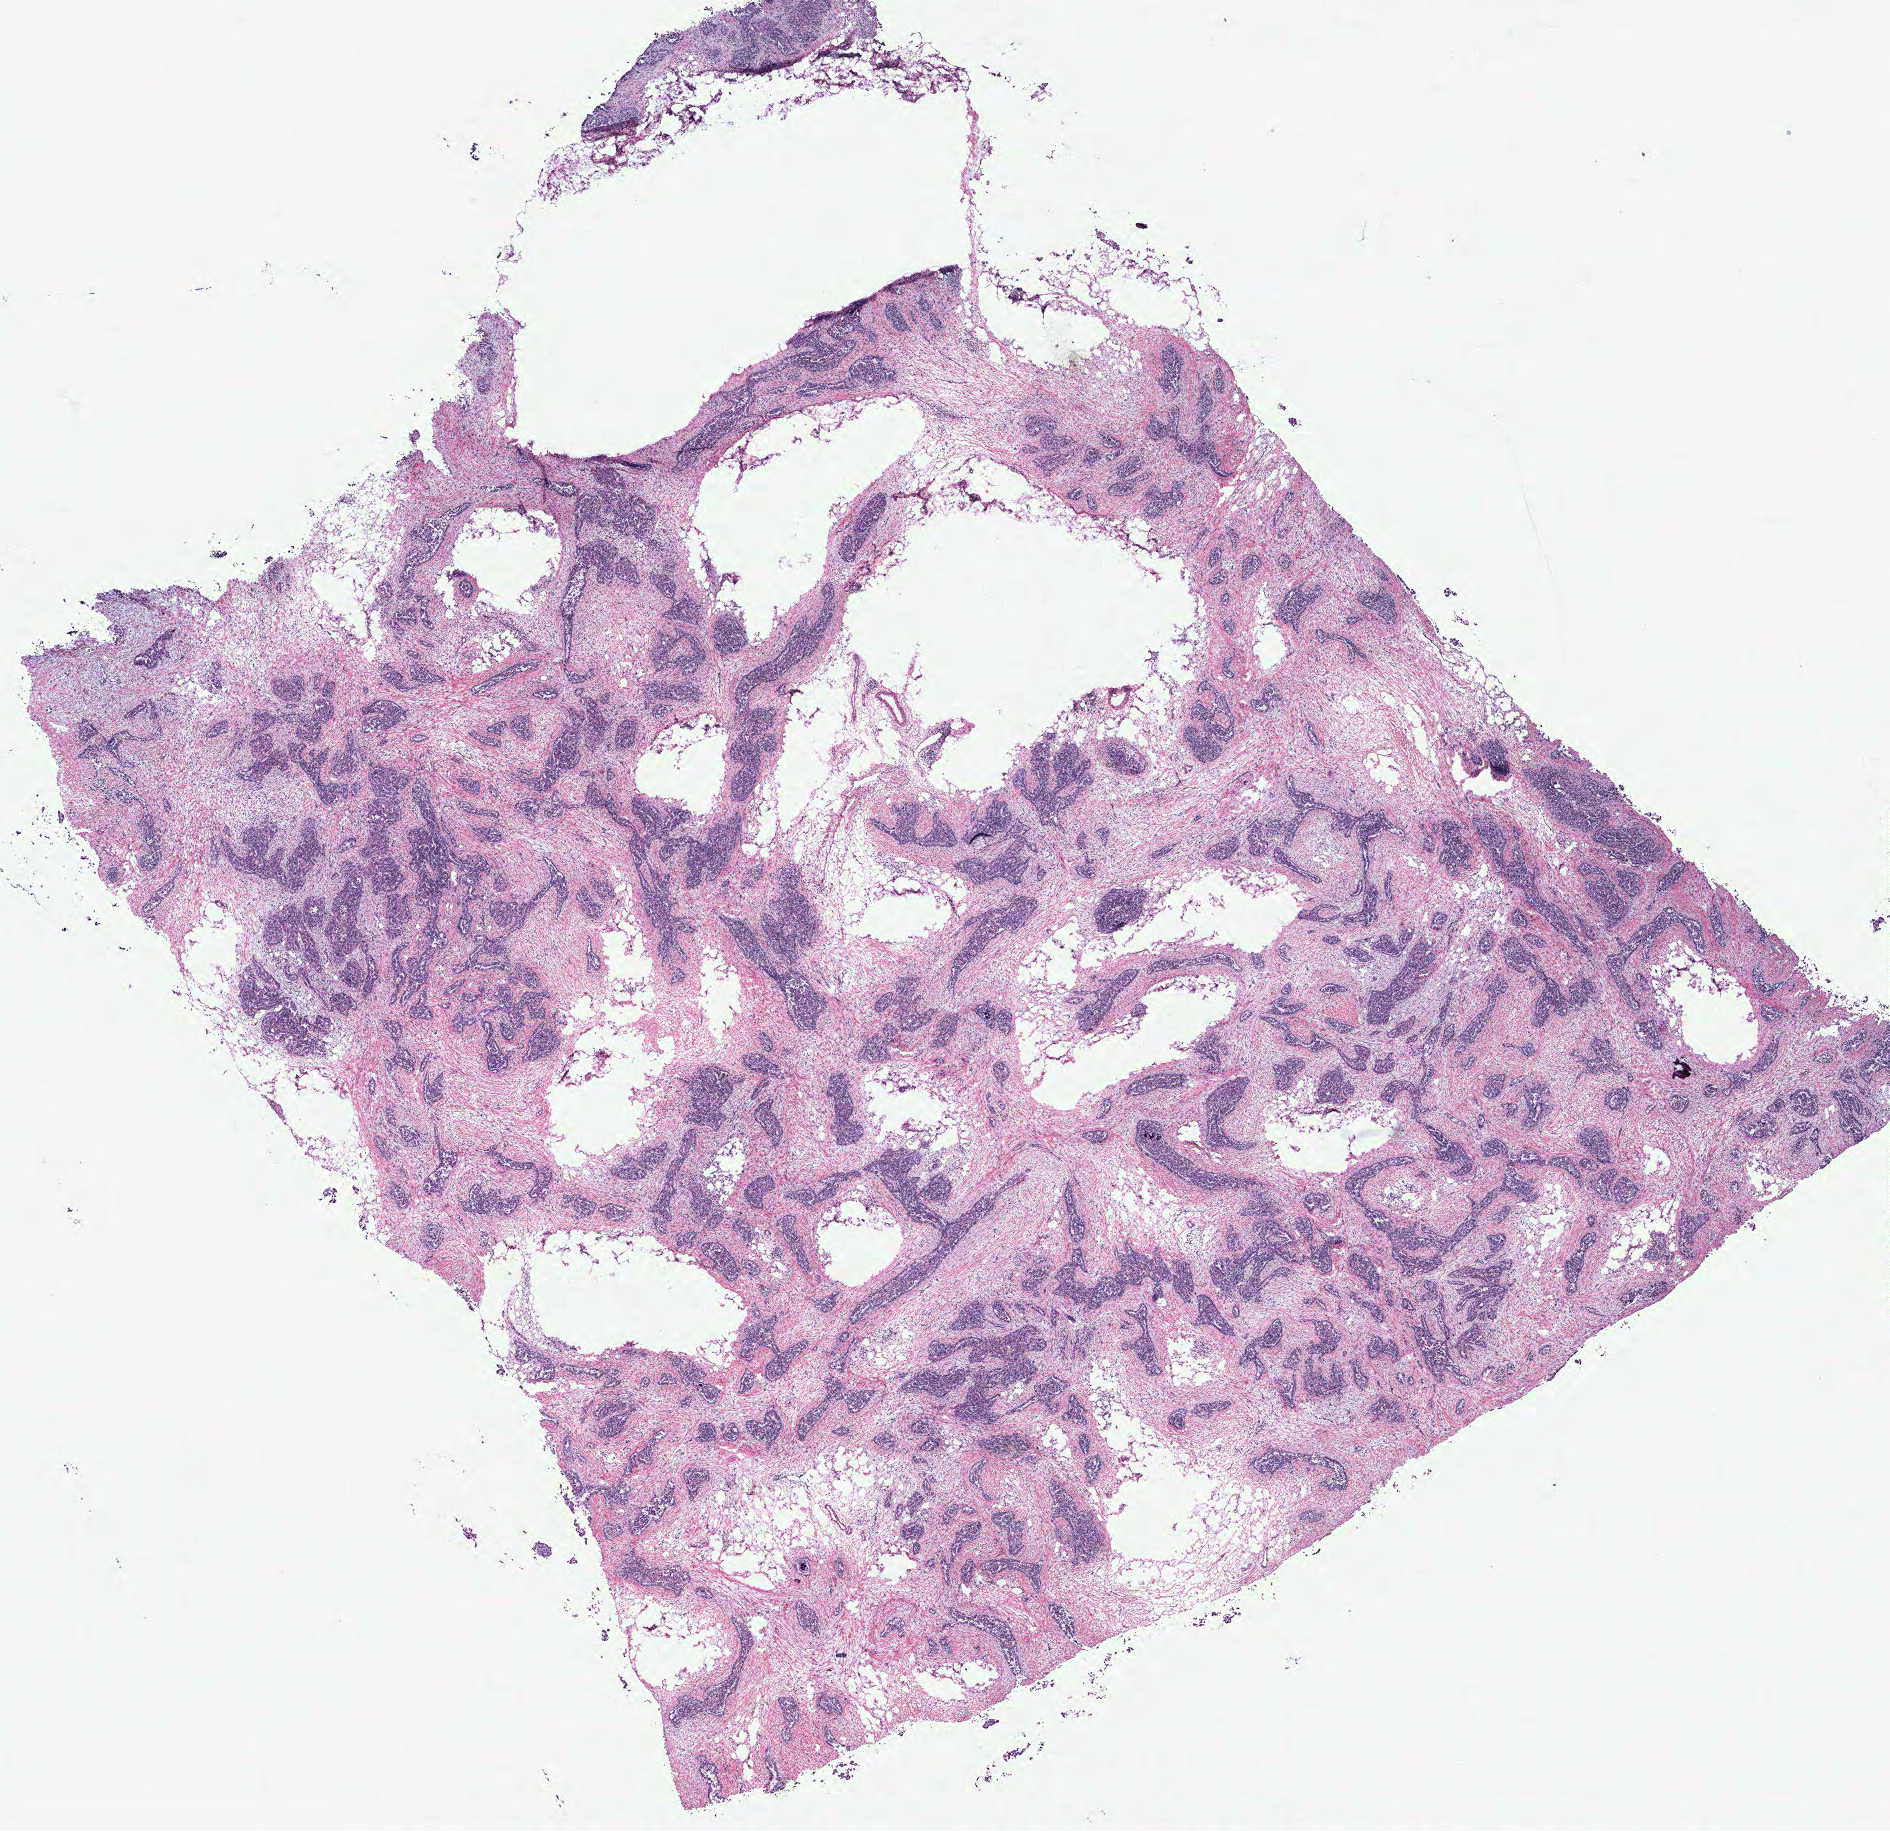
Digitized H&E-stained tissue section (whole slide), a low-resolution overview of the entire scanned area, about 15.1 x 14.7 mm; tumour tissue sample, ovary. Patient: female, age 57 years.
- primary tumour site (as recorded): ovary
- diagnosis: Serous adenocarcinoma, NOS